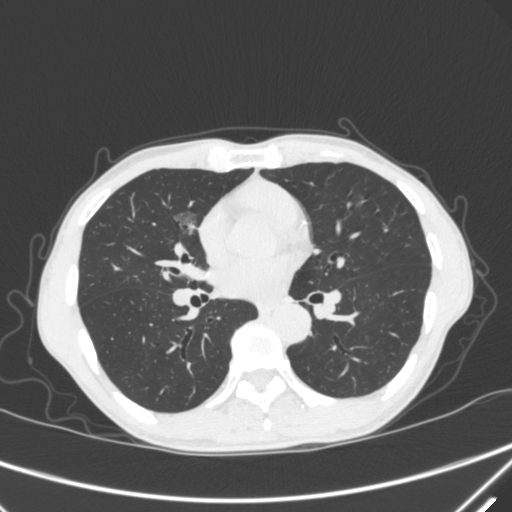
Chest CT, one axial slice. Position 168 of 340 along the scan axis. 120 kVp. Lung window (W 1500 / L -600 HU). 512 × 512 image matrix, field of view 350 × 350 mm. Patient: male, 67 years. Case-level facts recorded for this patient, not image findings: clinical TNM (as recorded): T1c N0 M0.
Annotated regions visible in this slice (rectangle marked by the reading radiologist):
- lung tumour (recorded histology: adenocarcinoma): bounding box [x1, y1, x2, y2] px = [167, 200, 196, 248]